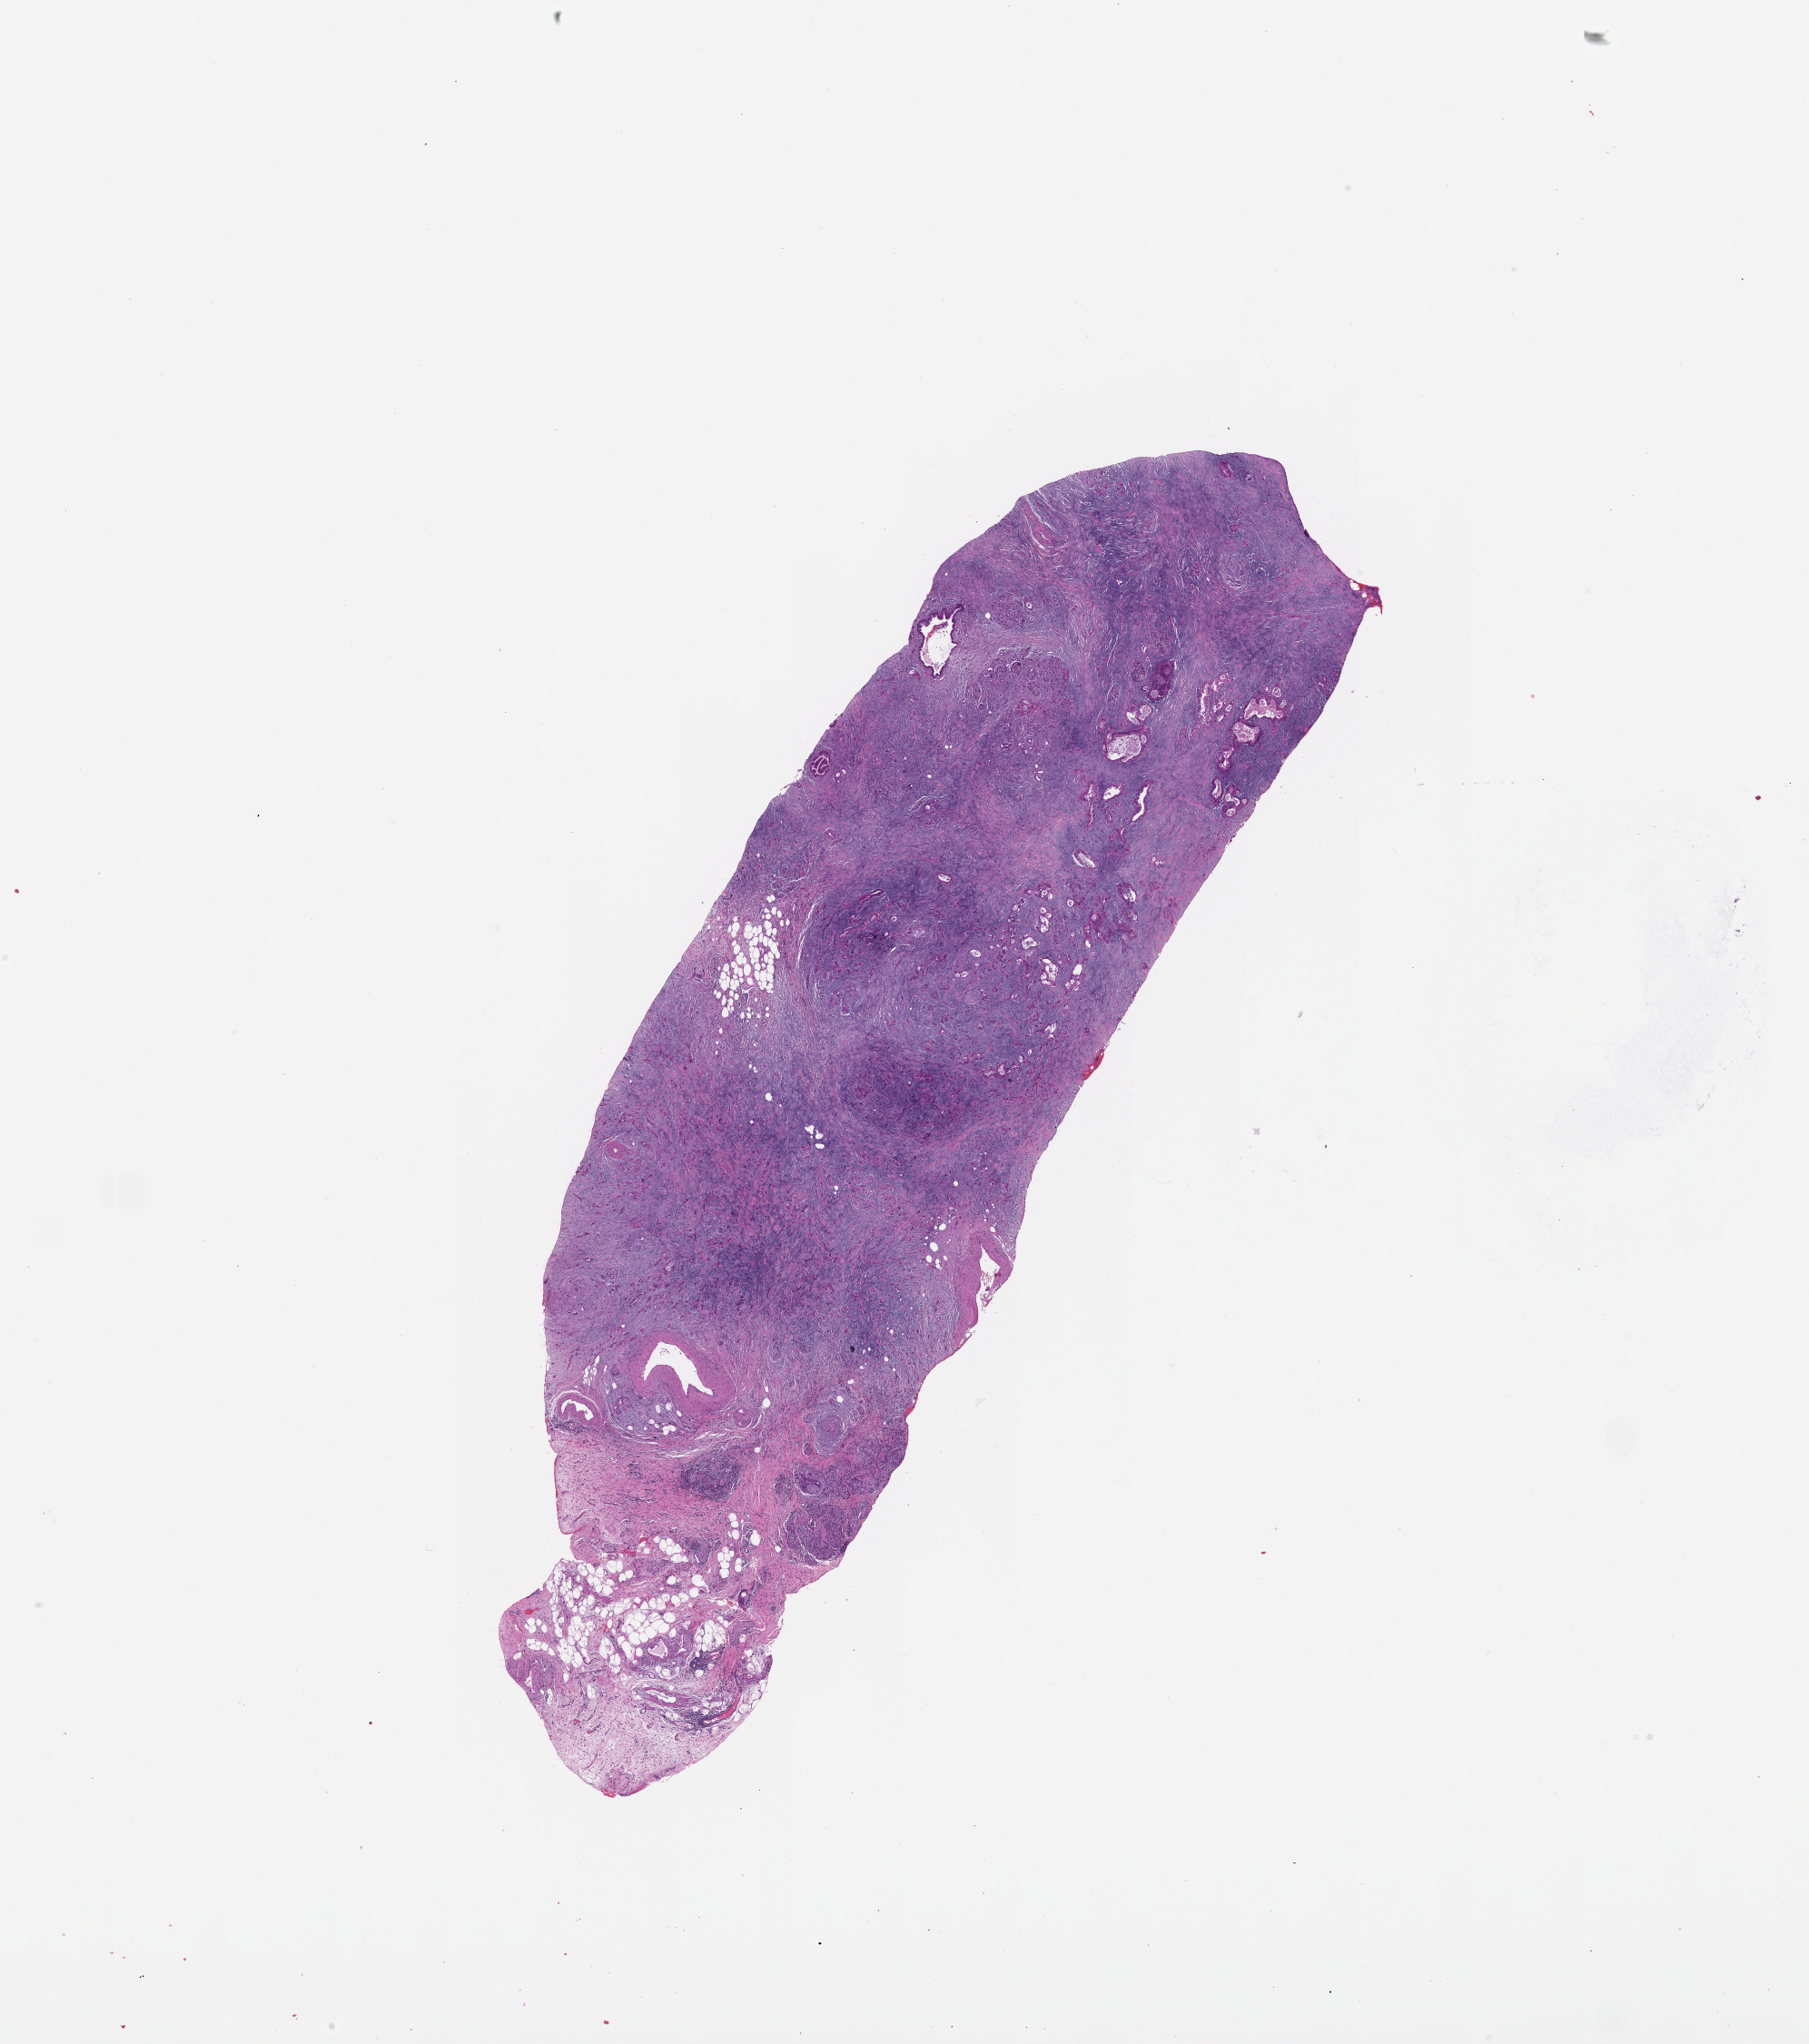
Digitized Hematoxylin and eosin (H&E) stained tissue section (whole slide), low-resolution overview of the scanned area, about 16.0 x 18.1 mm (from a 20x scan); pancreas, tumour tissue. Female, 71 y/o.
Diagnosis: Infiltrating duct carcinoma, NOS.